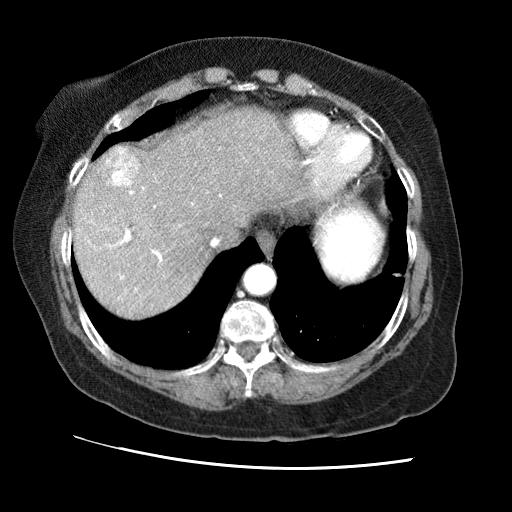
Contrast-enhanced abdominal CT (liver protocol), one axial slice. Position 56 of 65 along the scan axis. Reconstruction kernel STANDARD. 120 kVp. Soft-tissue window (W 400 / L 40 HU). 2.5 mm slice thickness. 512 × 512 image matrix, field of view 340 × 340 mm. From the clinical record (not read from this slice): diagnosis: hepatocellular carcinoma (patient treated with transarterial chemoembolisation; whether this scan precedes or follows treatment is not stated here); TNM stage (as recorded): Stage-II; Child-Pugh class: A; tumour differentiation: no biopsy; tumour nodularity: multinodular.
Structures marked on this image (semi-automatic segmentation, software-assisted and operator-edited):
- abdominal aorta: bounding box (x1, y1, x2, y2) in pixels: (245, 265, 274, 293)
- liver parenchyma outside the tumour (the mass and vessels are separate outlines, so this box may not span the whole liver): (72, 108, 312, 316)
- mass: (101, 147, 137, 186)
- liver vessels: (88, 162, 306, 290)